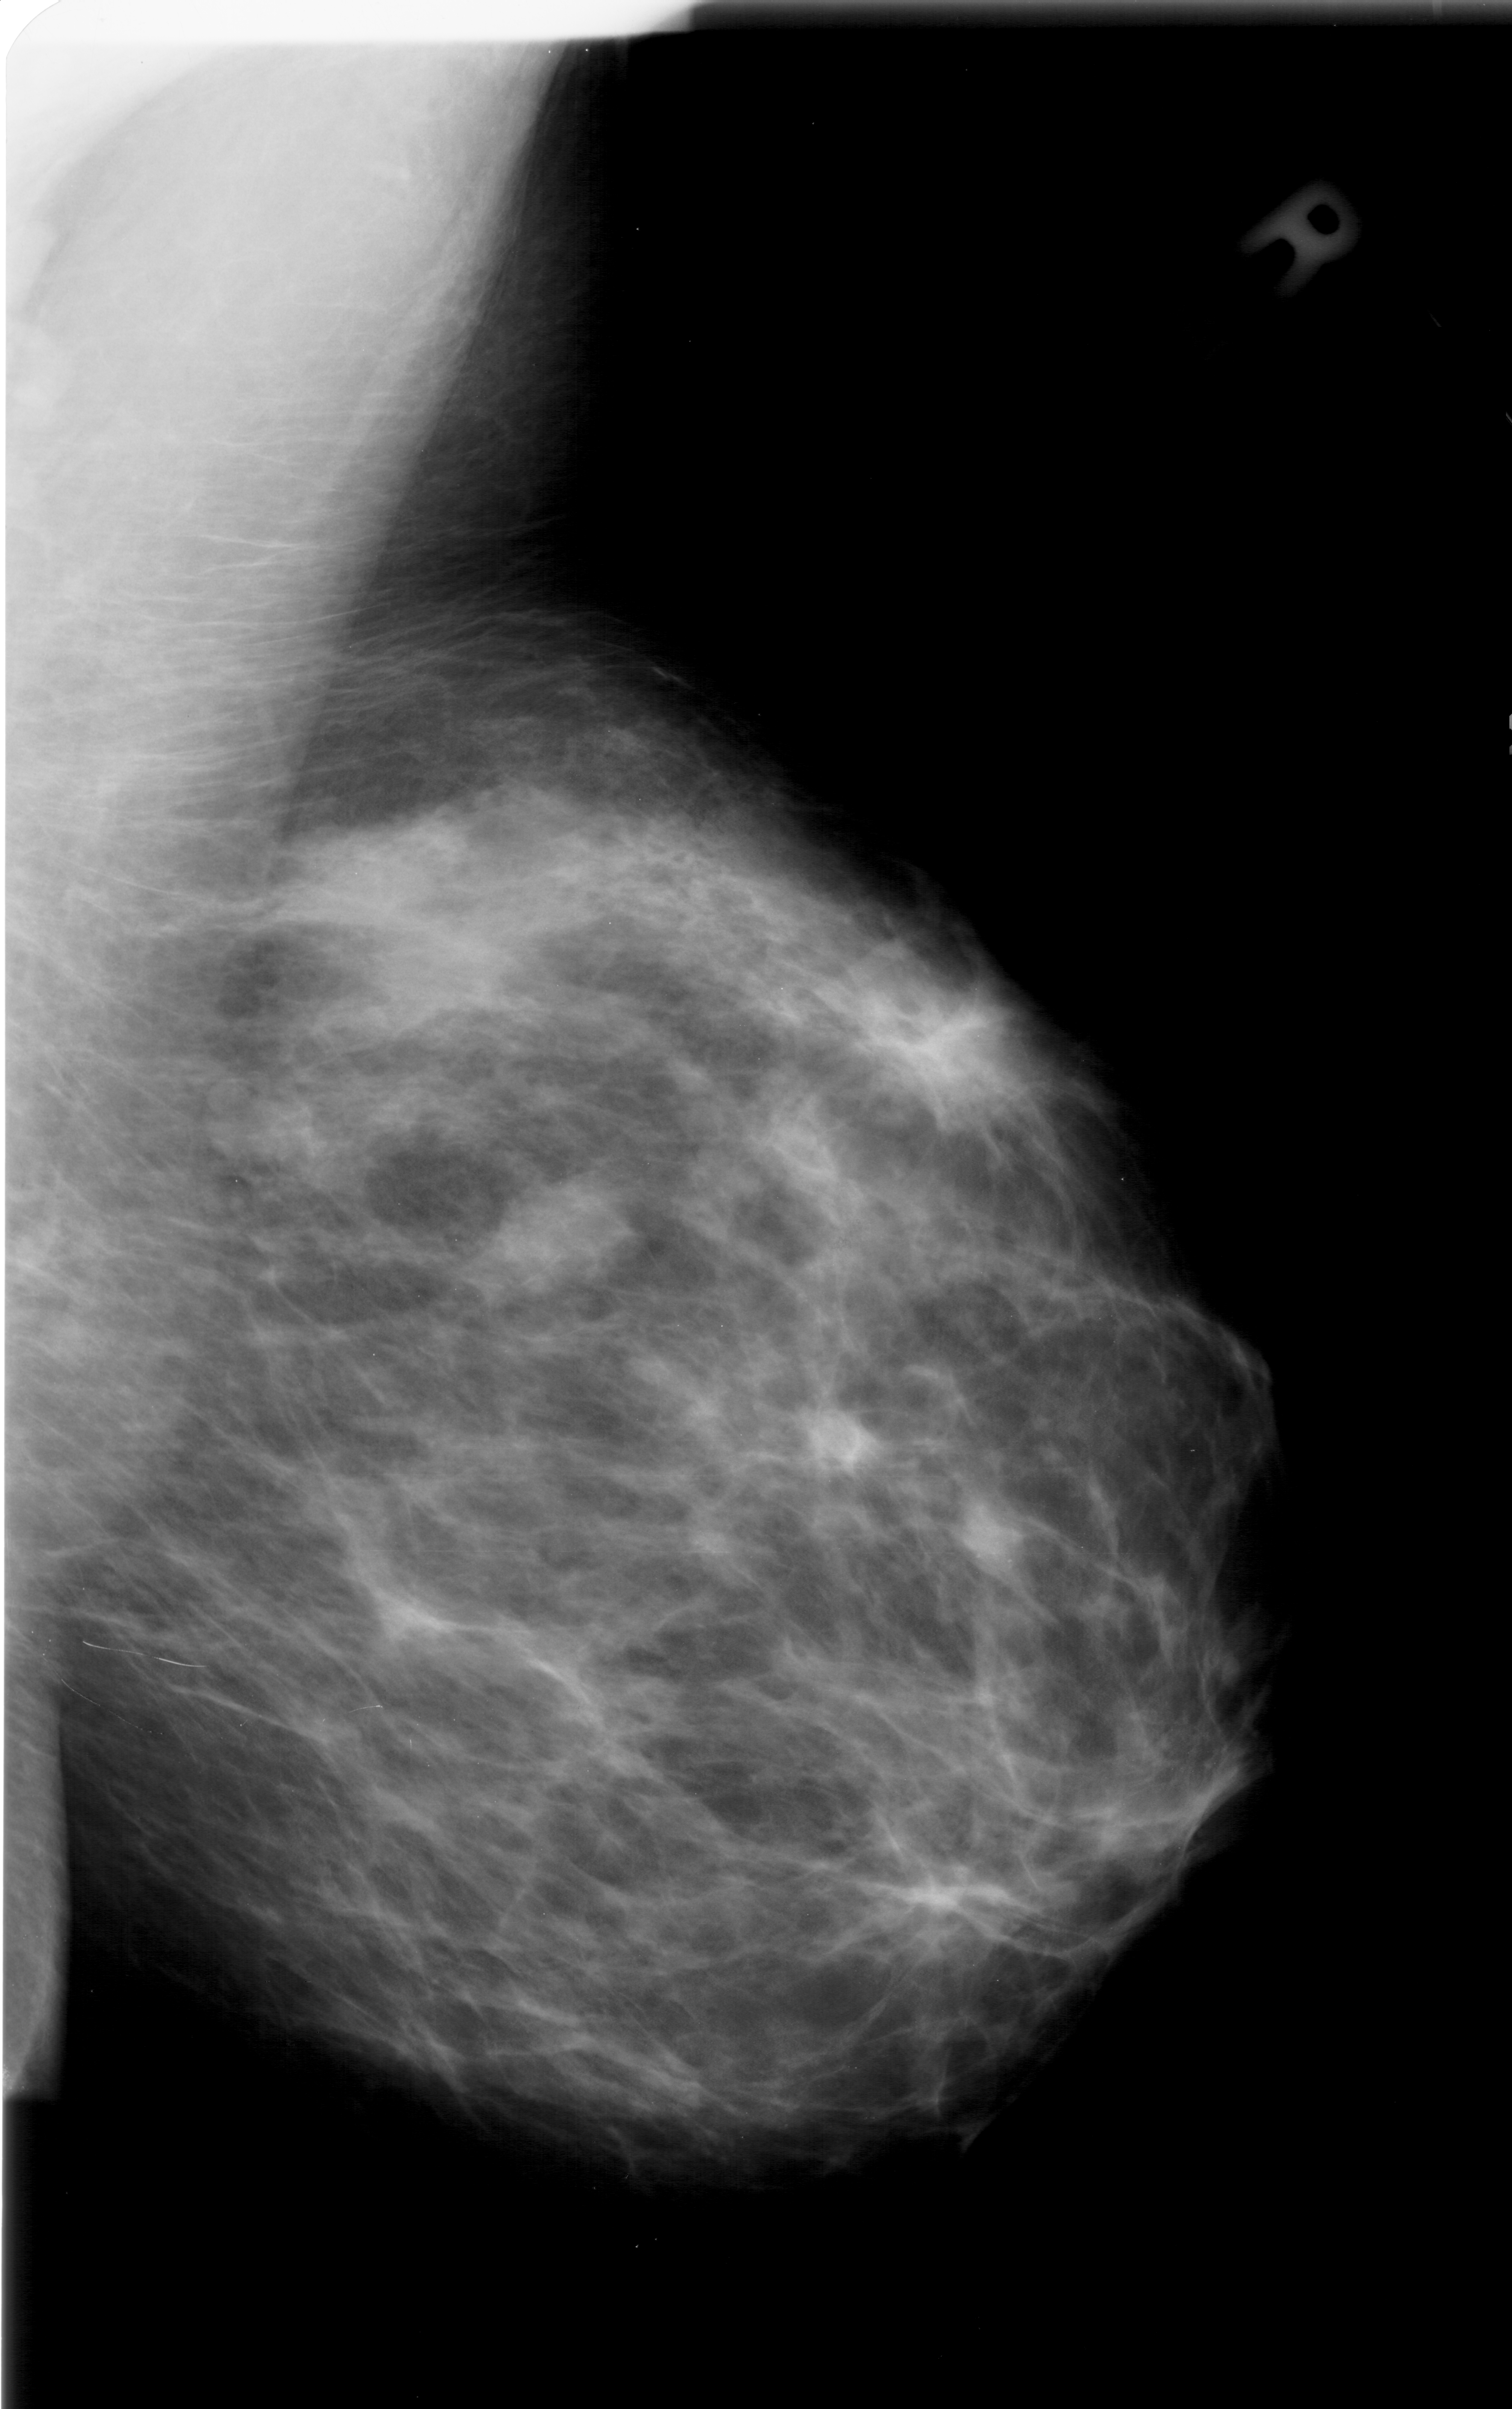
Mammogram (digitized film). Right breast. Mediolateral oblique (MLO) view. Breast composition: almost entirely fatty (BI-RADS density category 1 of 4). 1512 × 2409 image matrix.
Expert-marked regions of interest on this film, with their recorded descriptors:
- mass, shape lobulated, margins ill defined; BI-RADS assessment category 4; pathology result (as recorded, not read from the image): benign: bounding box (x1, y1, x2, y2) in pixels: (490, 1187, 621, 1296)